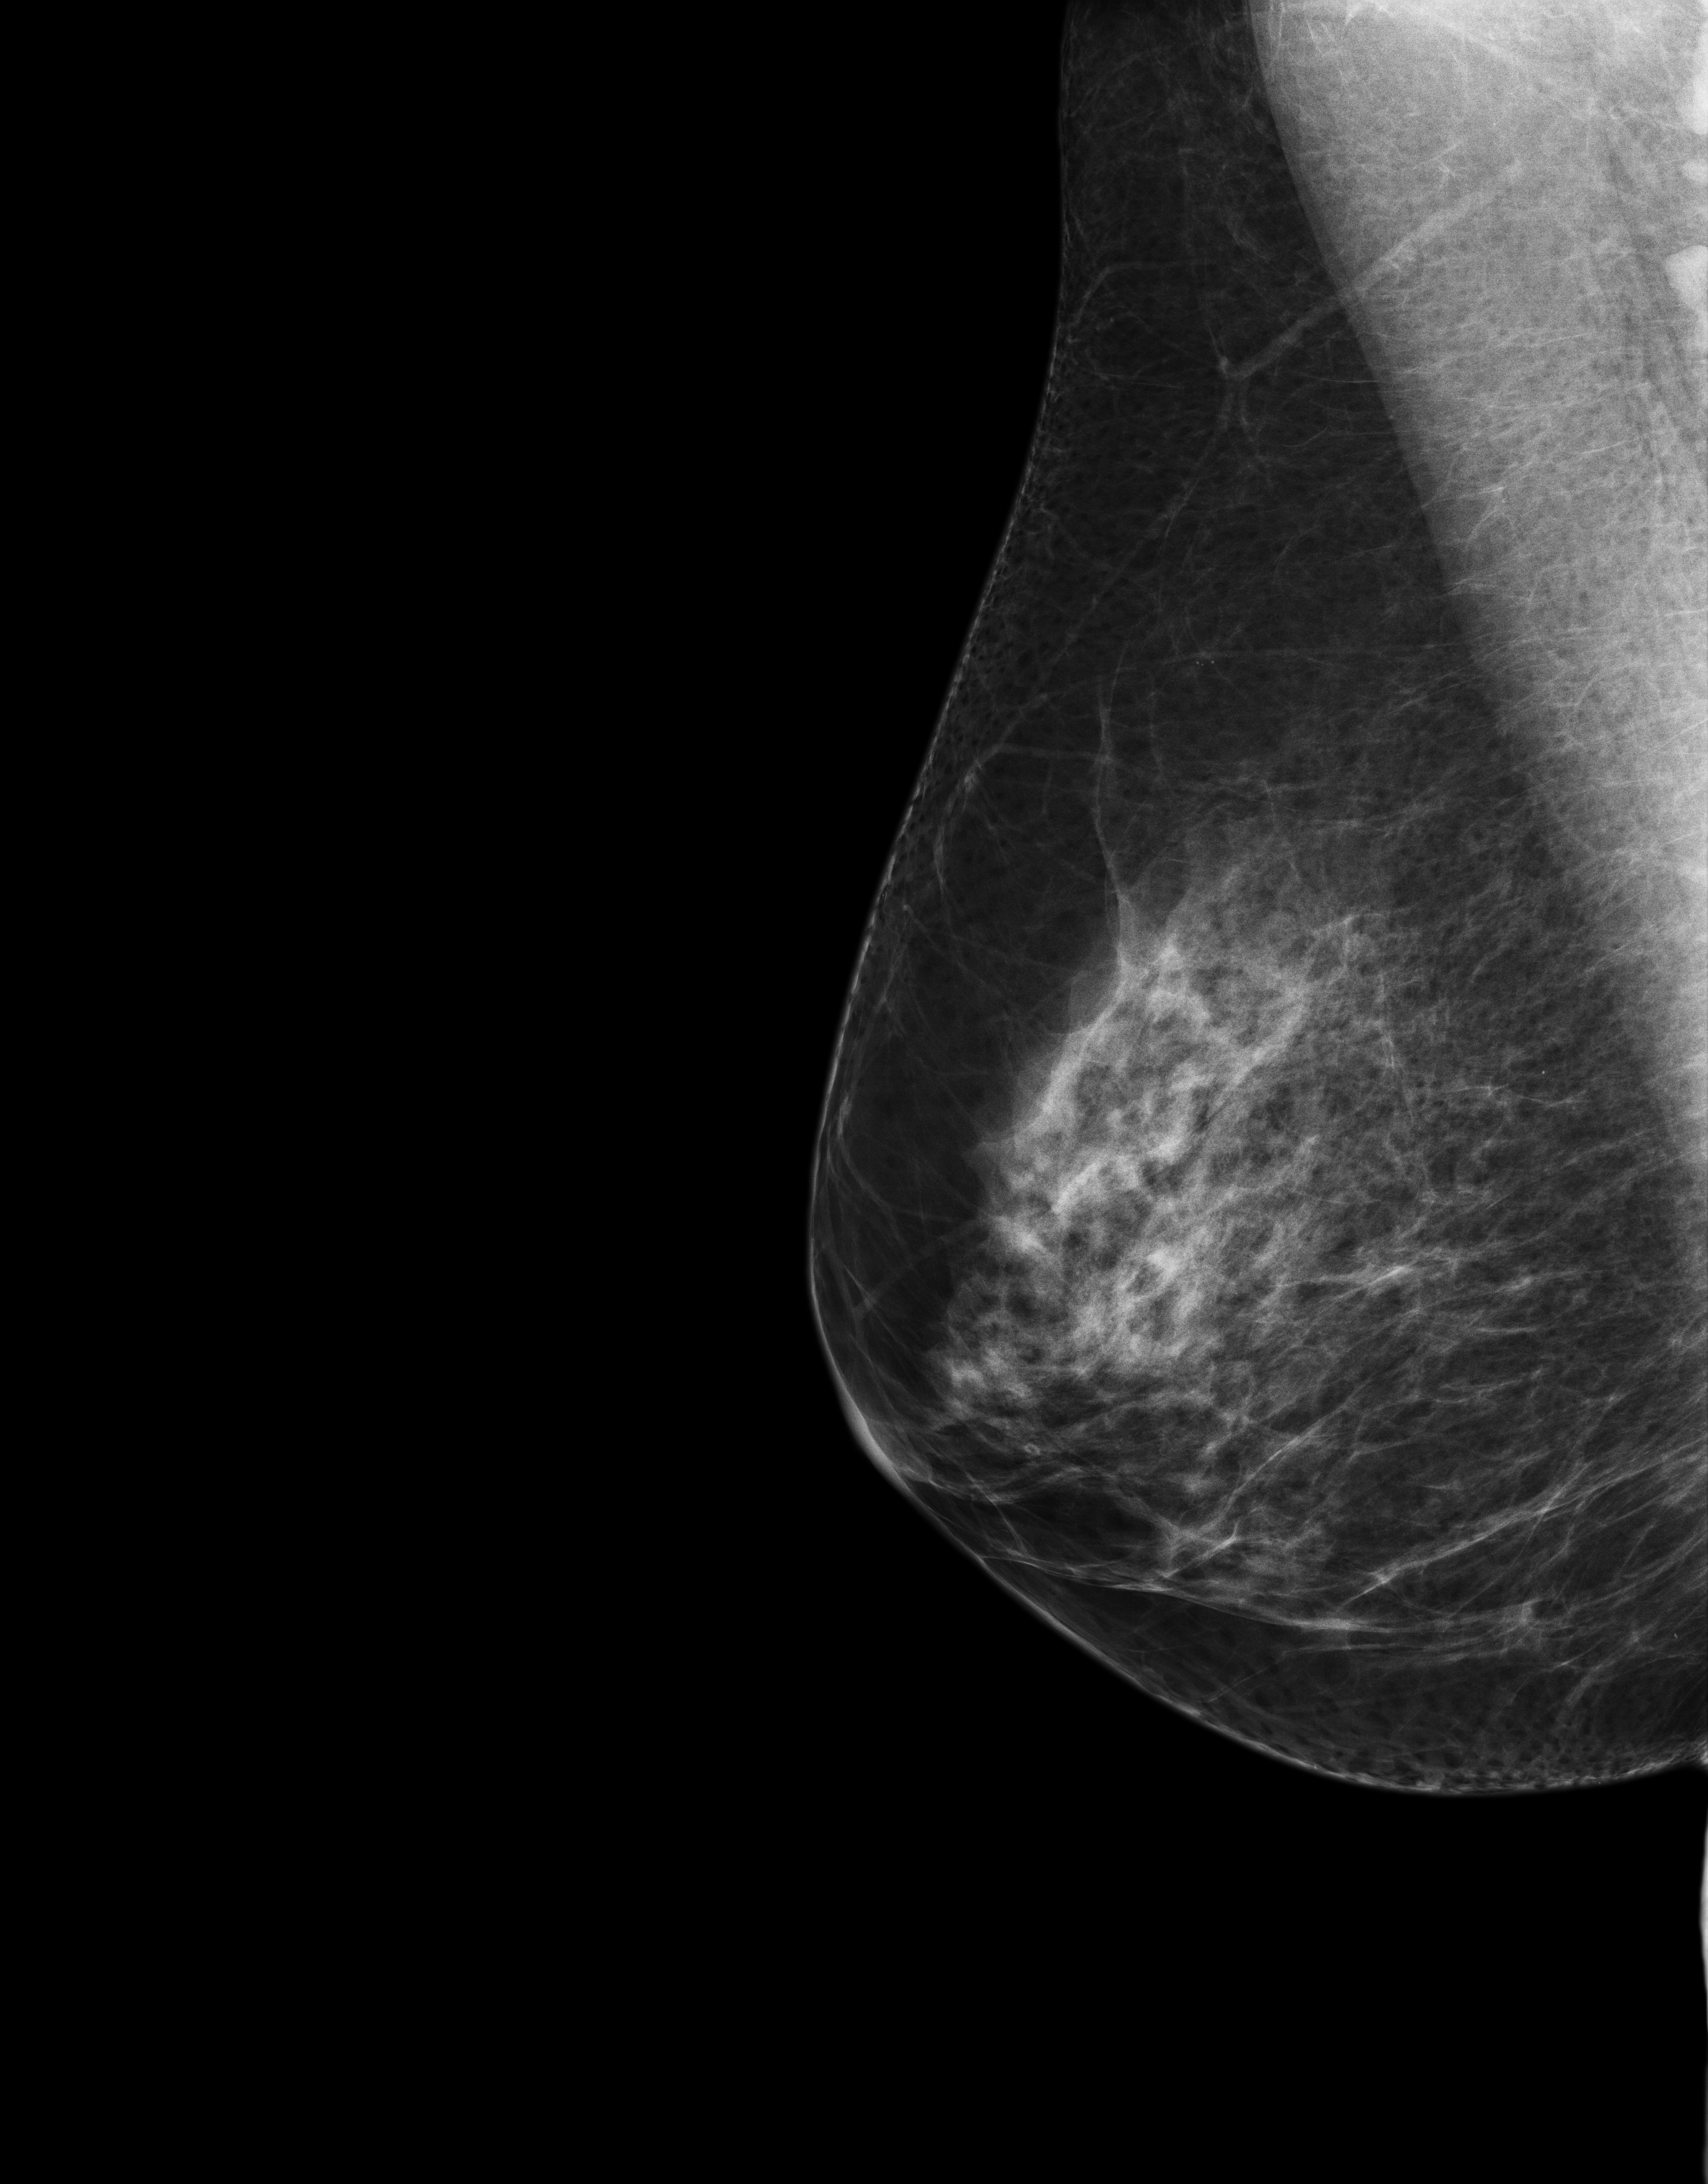
Full-field digital mammogram (FFDM); right breast; medio-lateral oblique projection; screening examination; compressed breast thickness 67 mm. Patient: female, 57 years.
Breast density at the screening exam (both breasts): scattered fibroglandular densities (BI-RADS density category b). Final BI-RADS category for the screening round (tomosynthesis exam, both breasts): category 1. Recall: no recall after this screen.